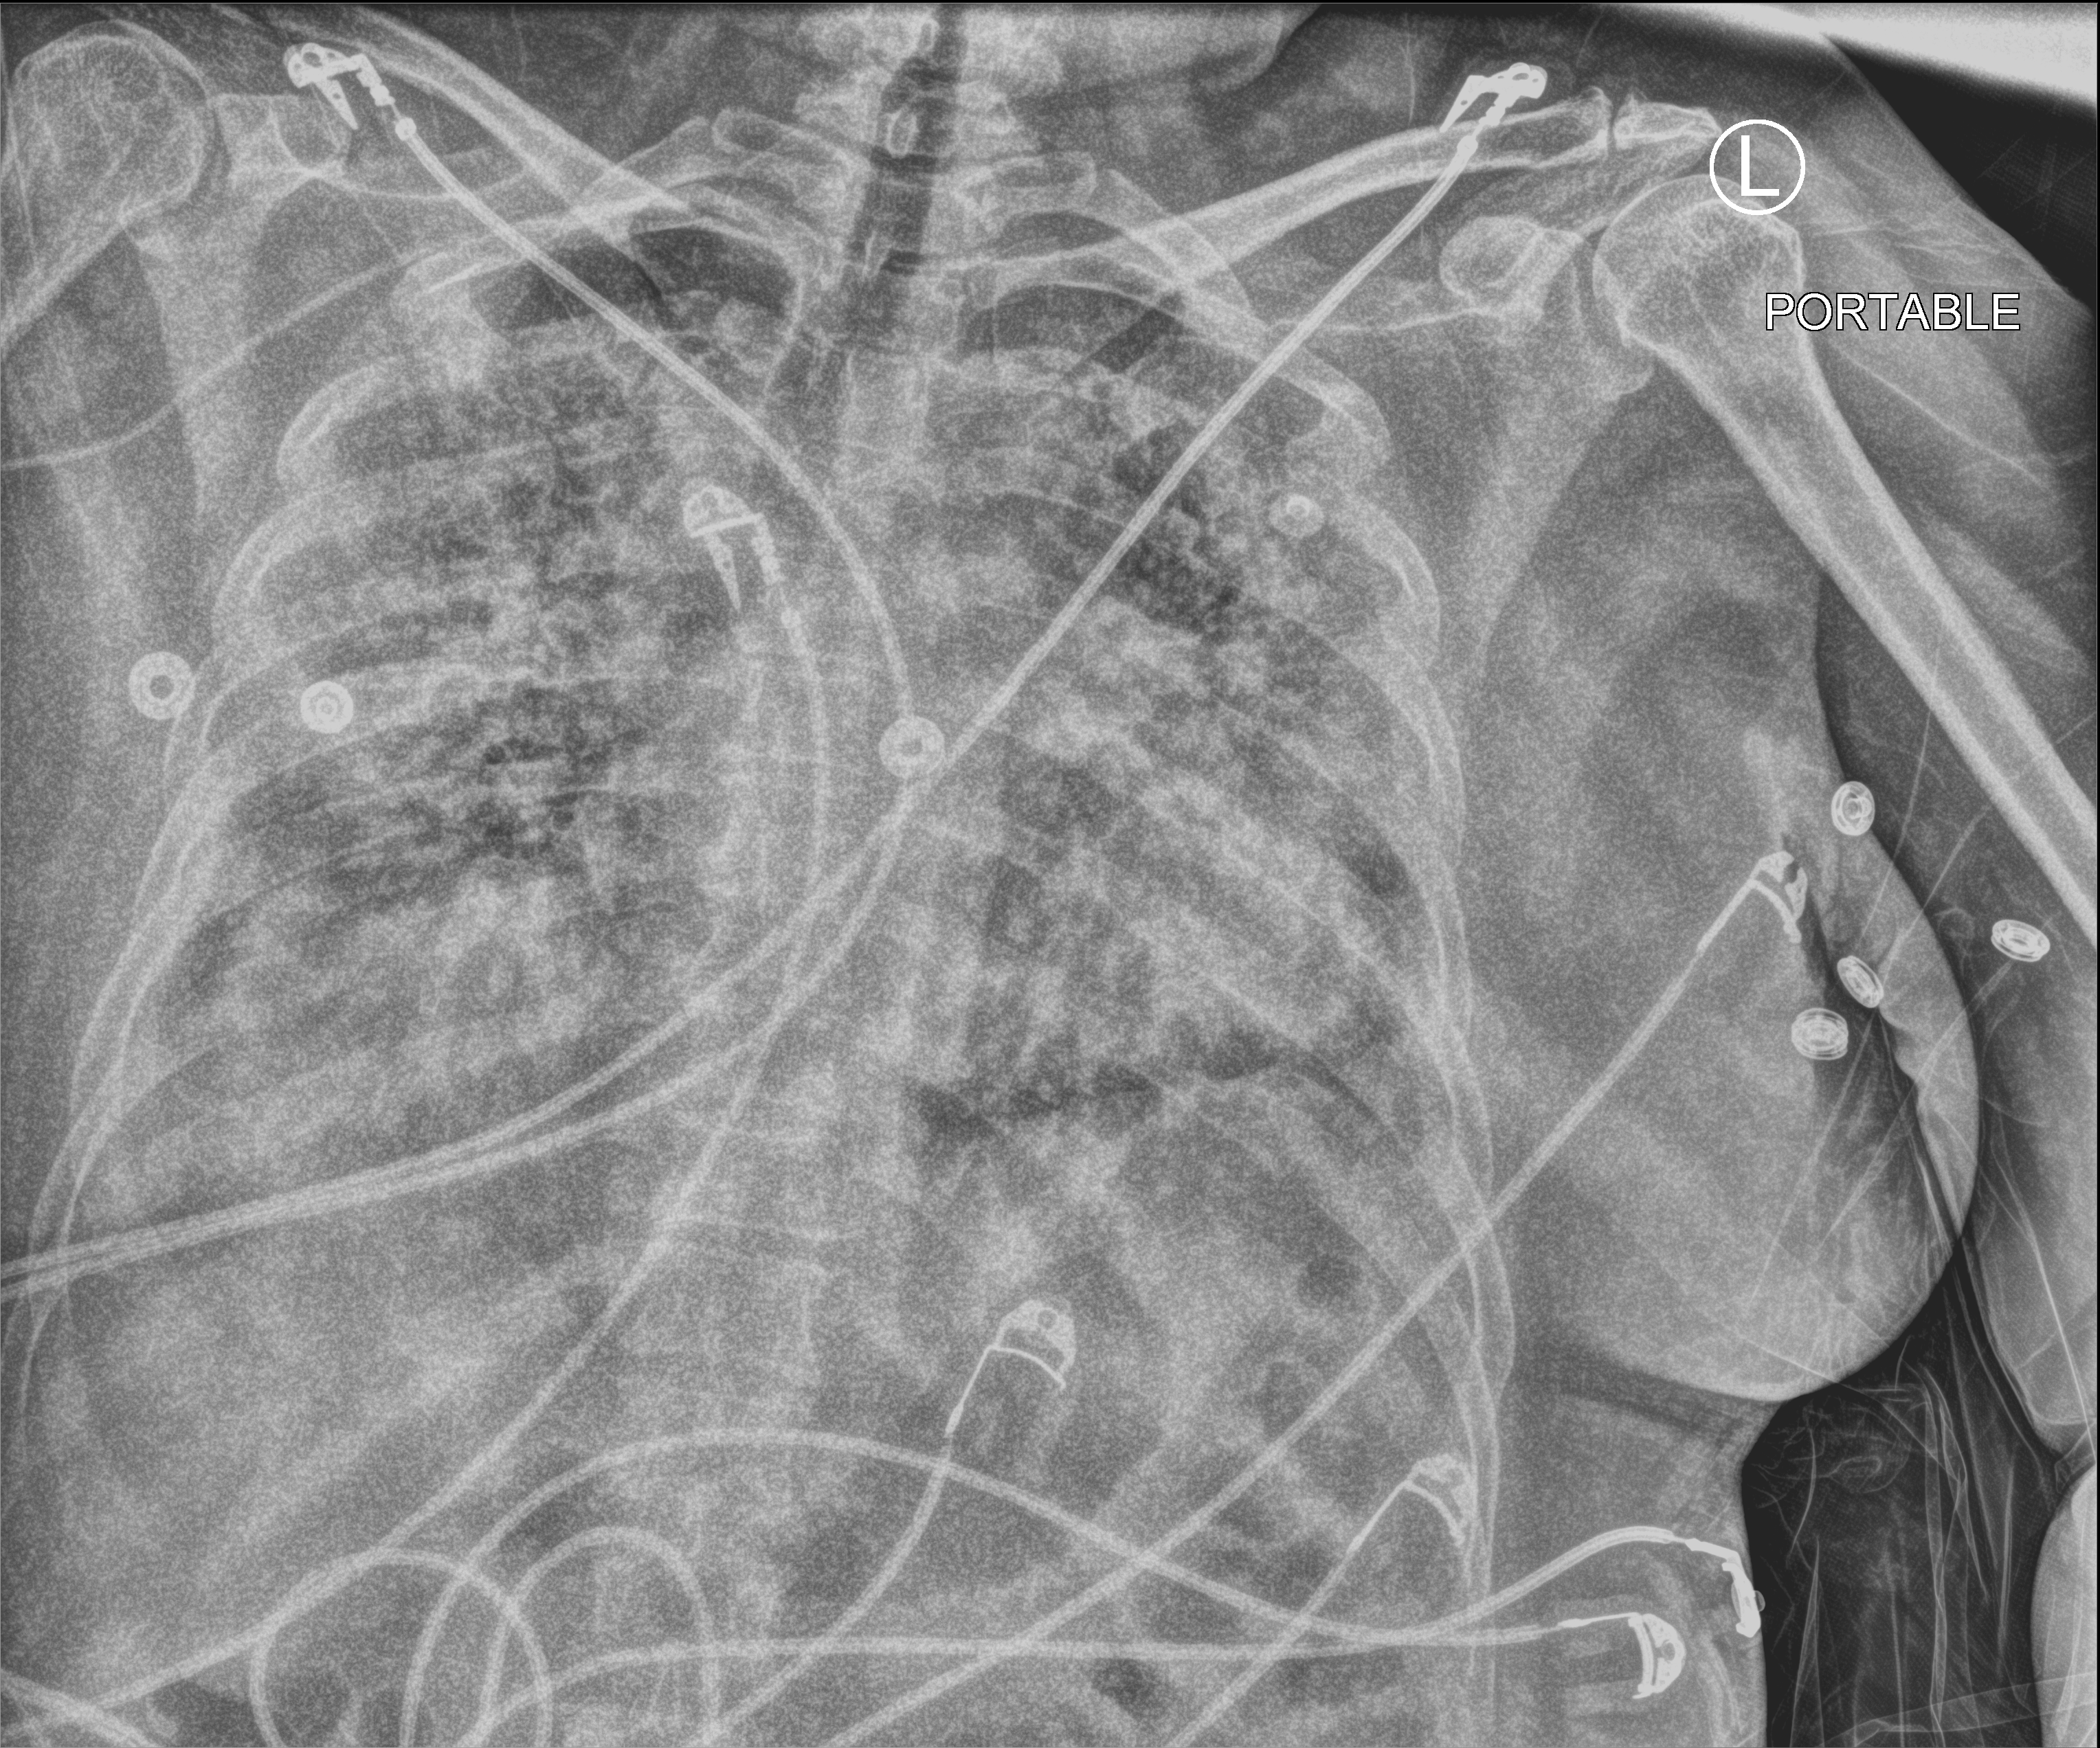
Bedside chest radiograph (computed radiography). Patient hospitalised with COVID-19; female, aged 18–59 years.
From the hospital-stay record, not from the radiograph (when in the stay this image was taken is not recorded):
- other chronic lung disease (admission record): no